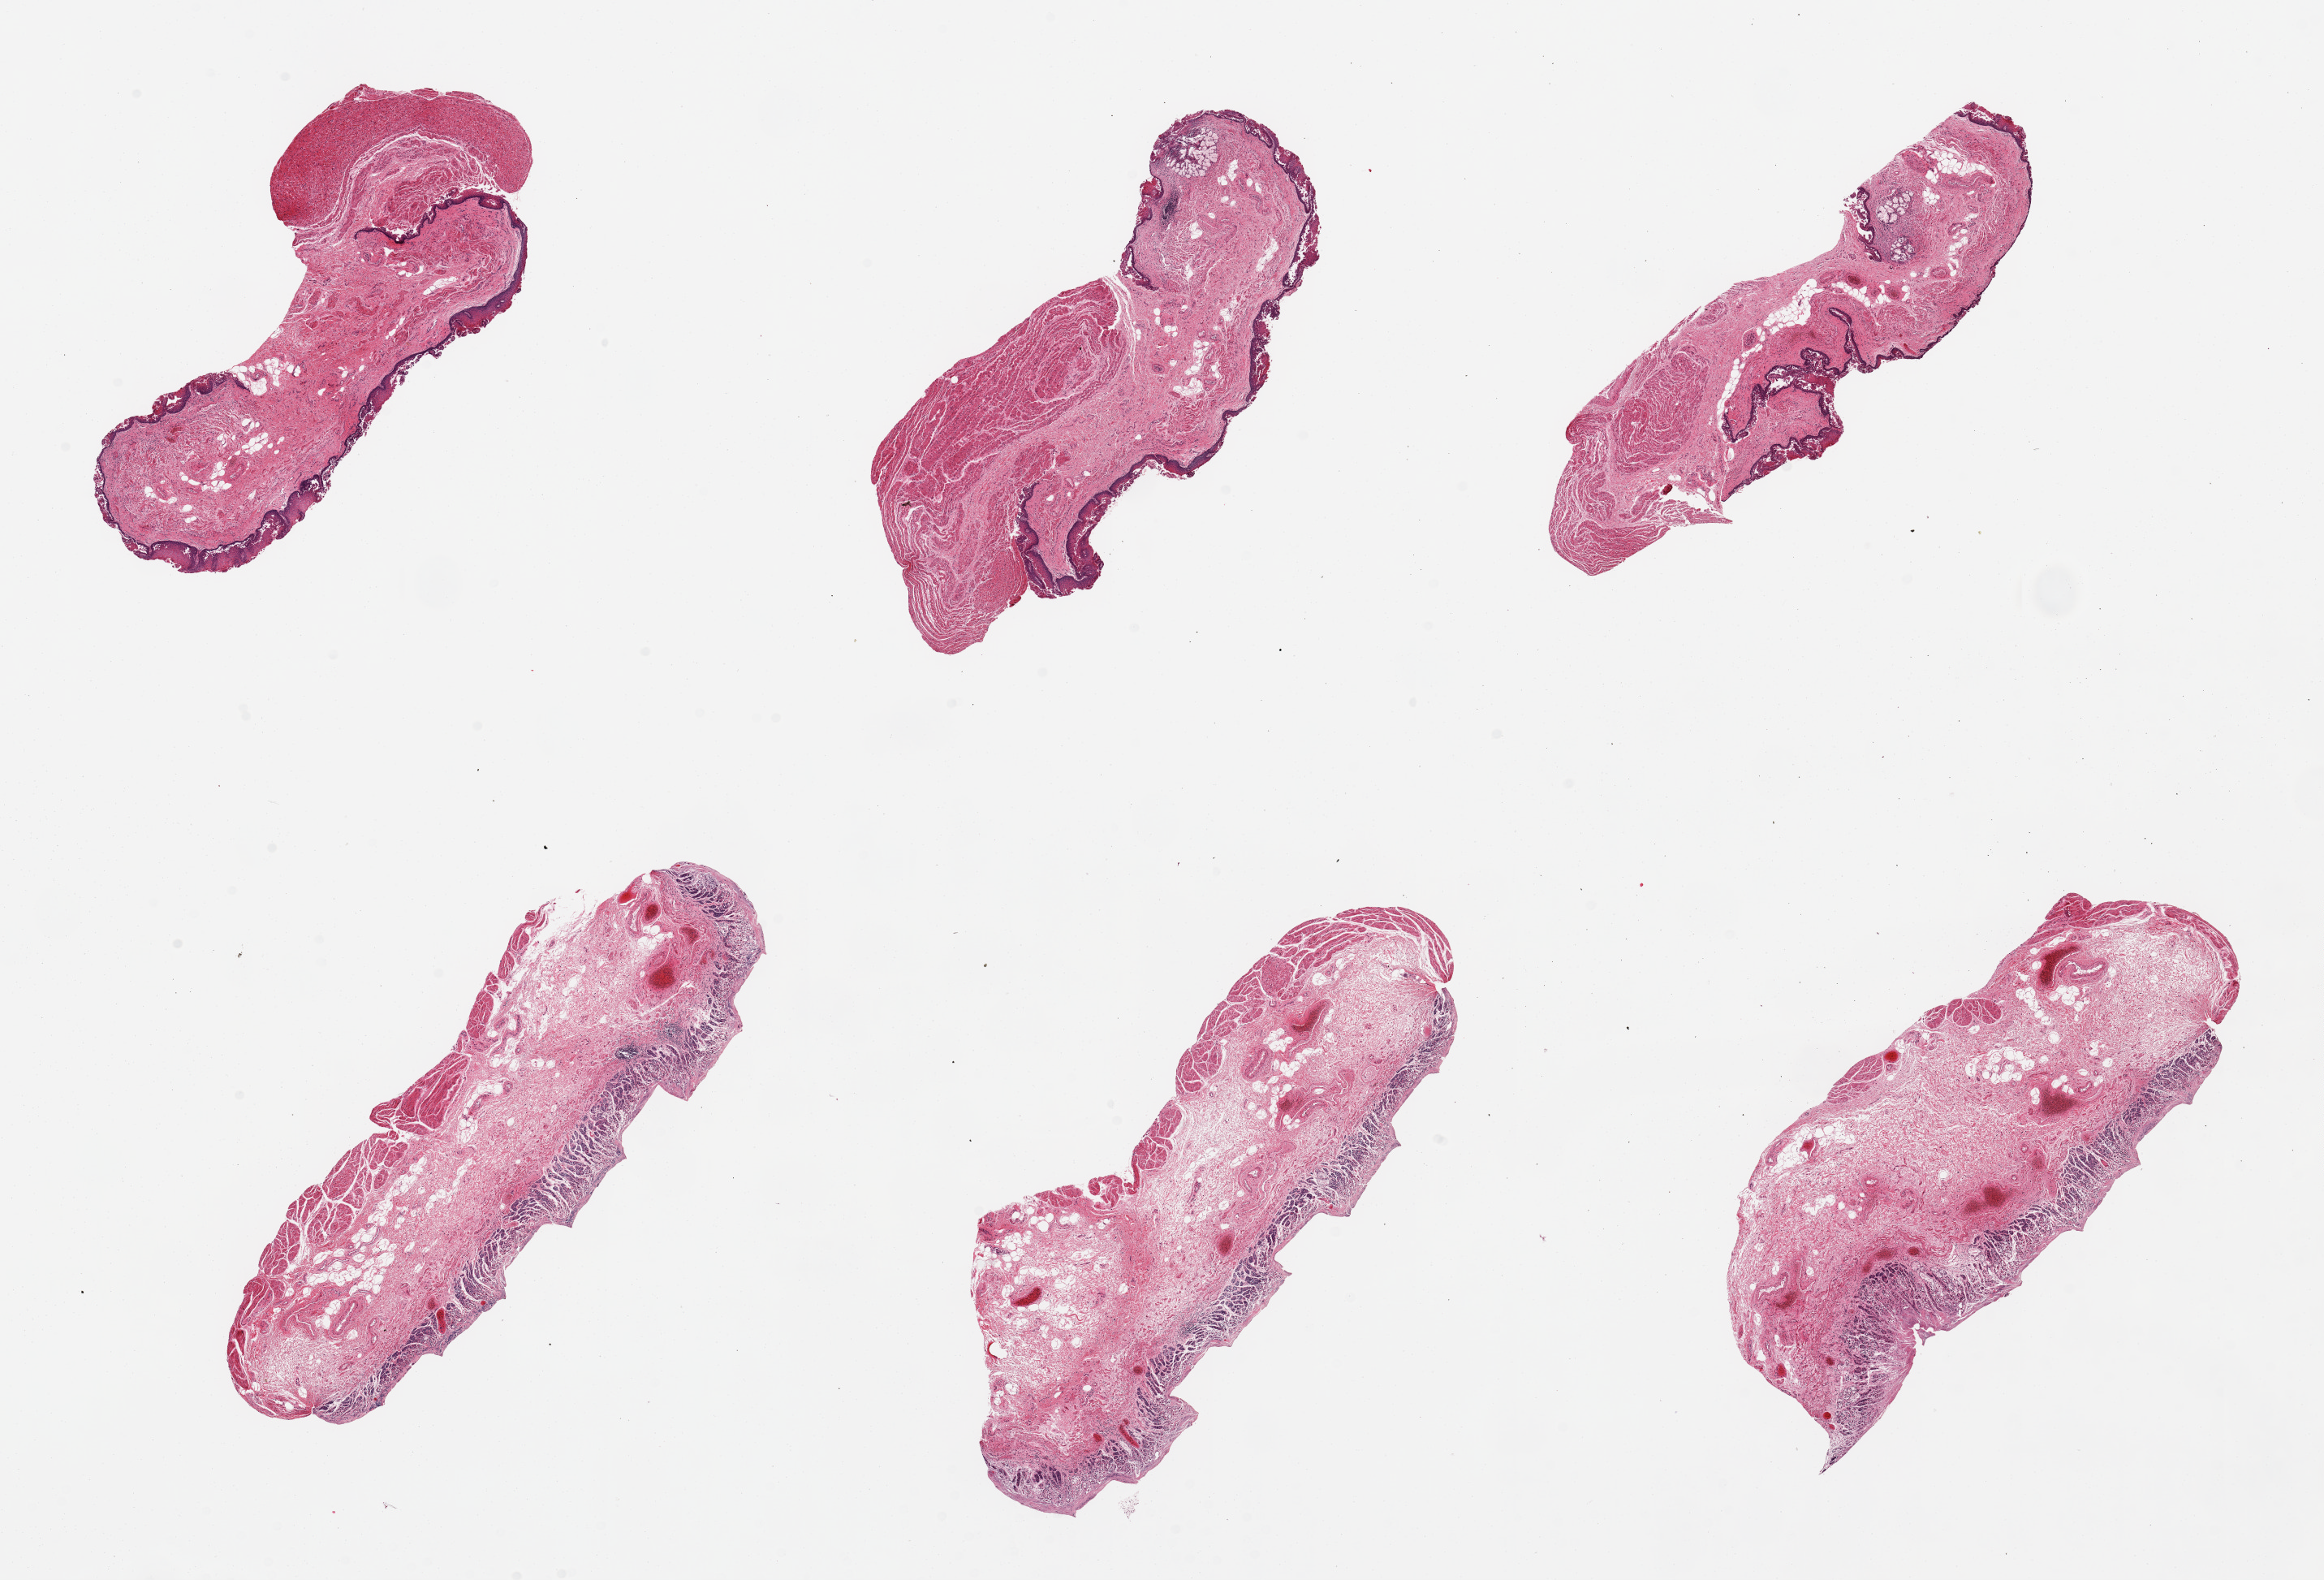
H&E whole-slide image — whole scanned area (about 22.6 x 15.4 mm) shown as a low-resolution overview. PAXgene-fixed paraffin-embedded (PFPE) section. Section of gastroesophageal junction (target tissue). Tissue donor sample. Donor: female.
Reviewer comment on this tissue sample: 6 pieces; 3 gastric and 3 esophageal mucosal specimens.